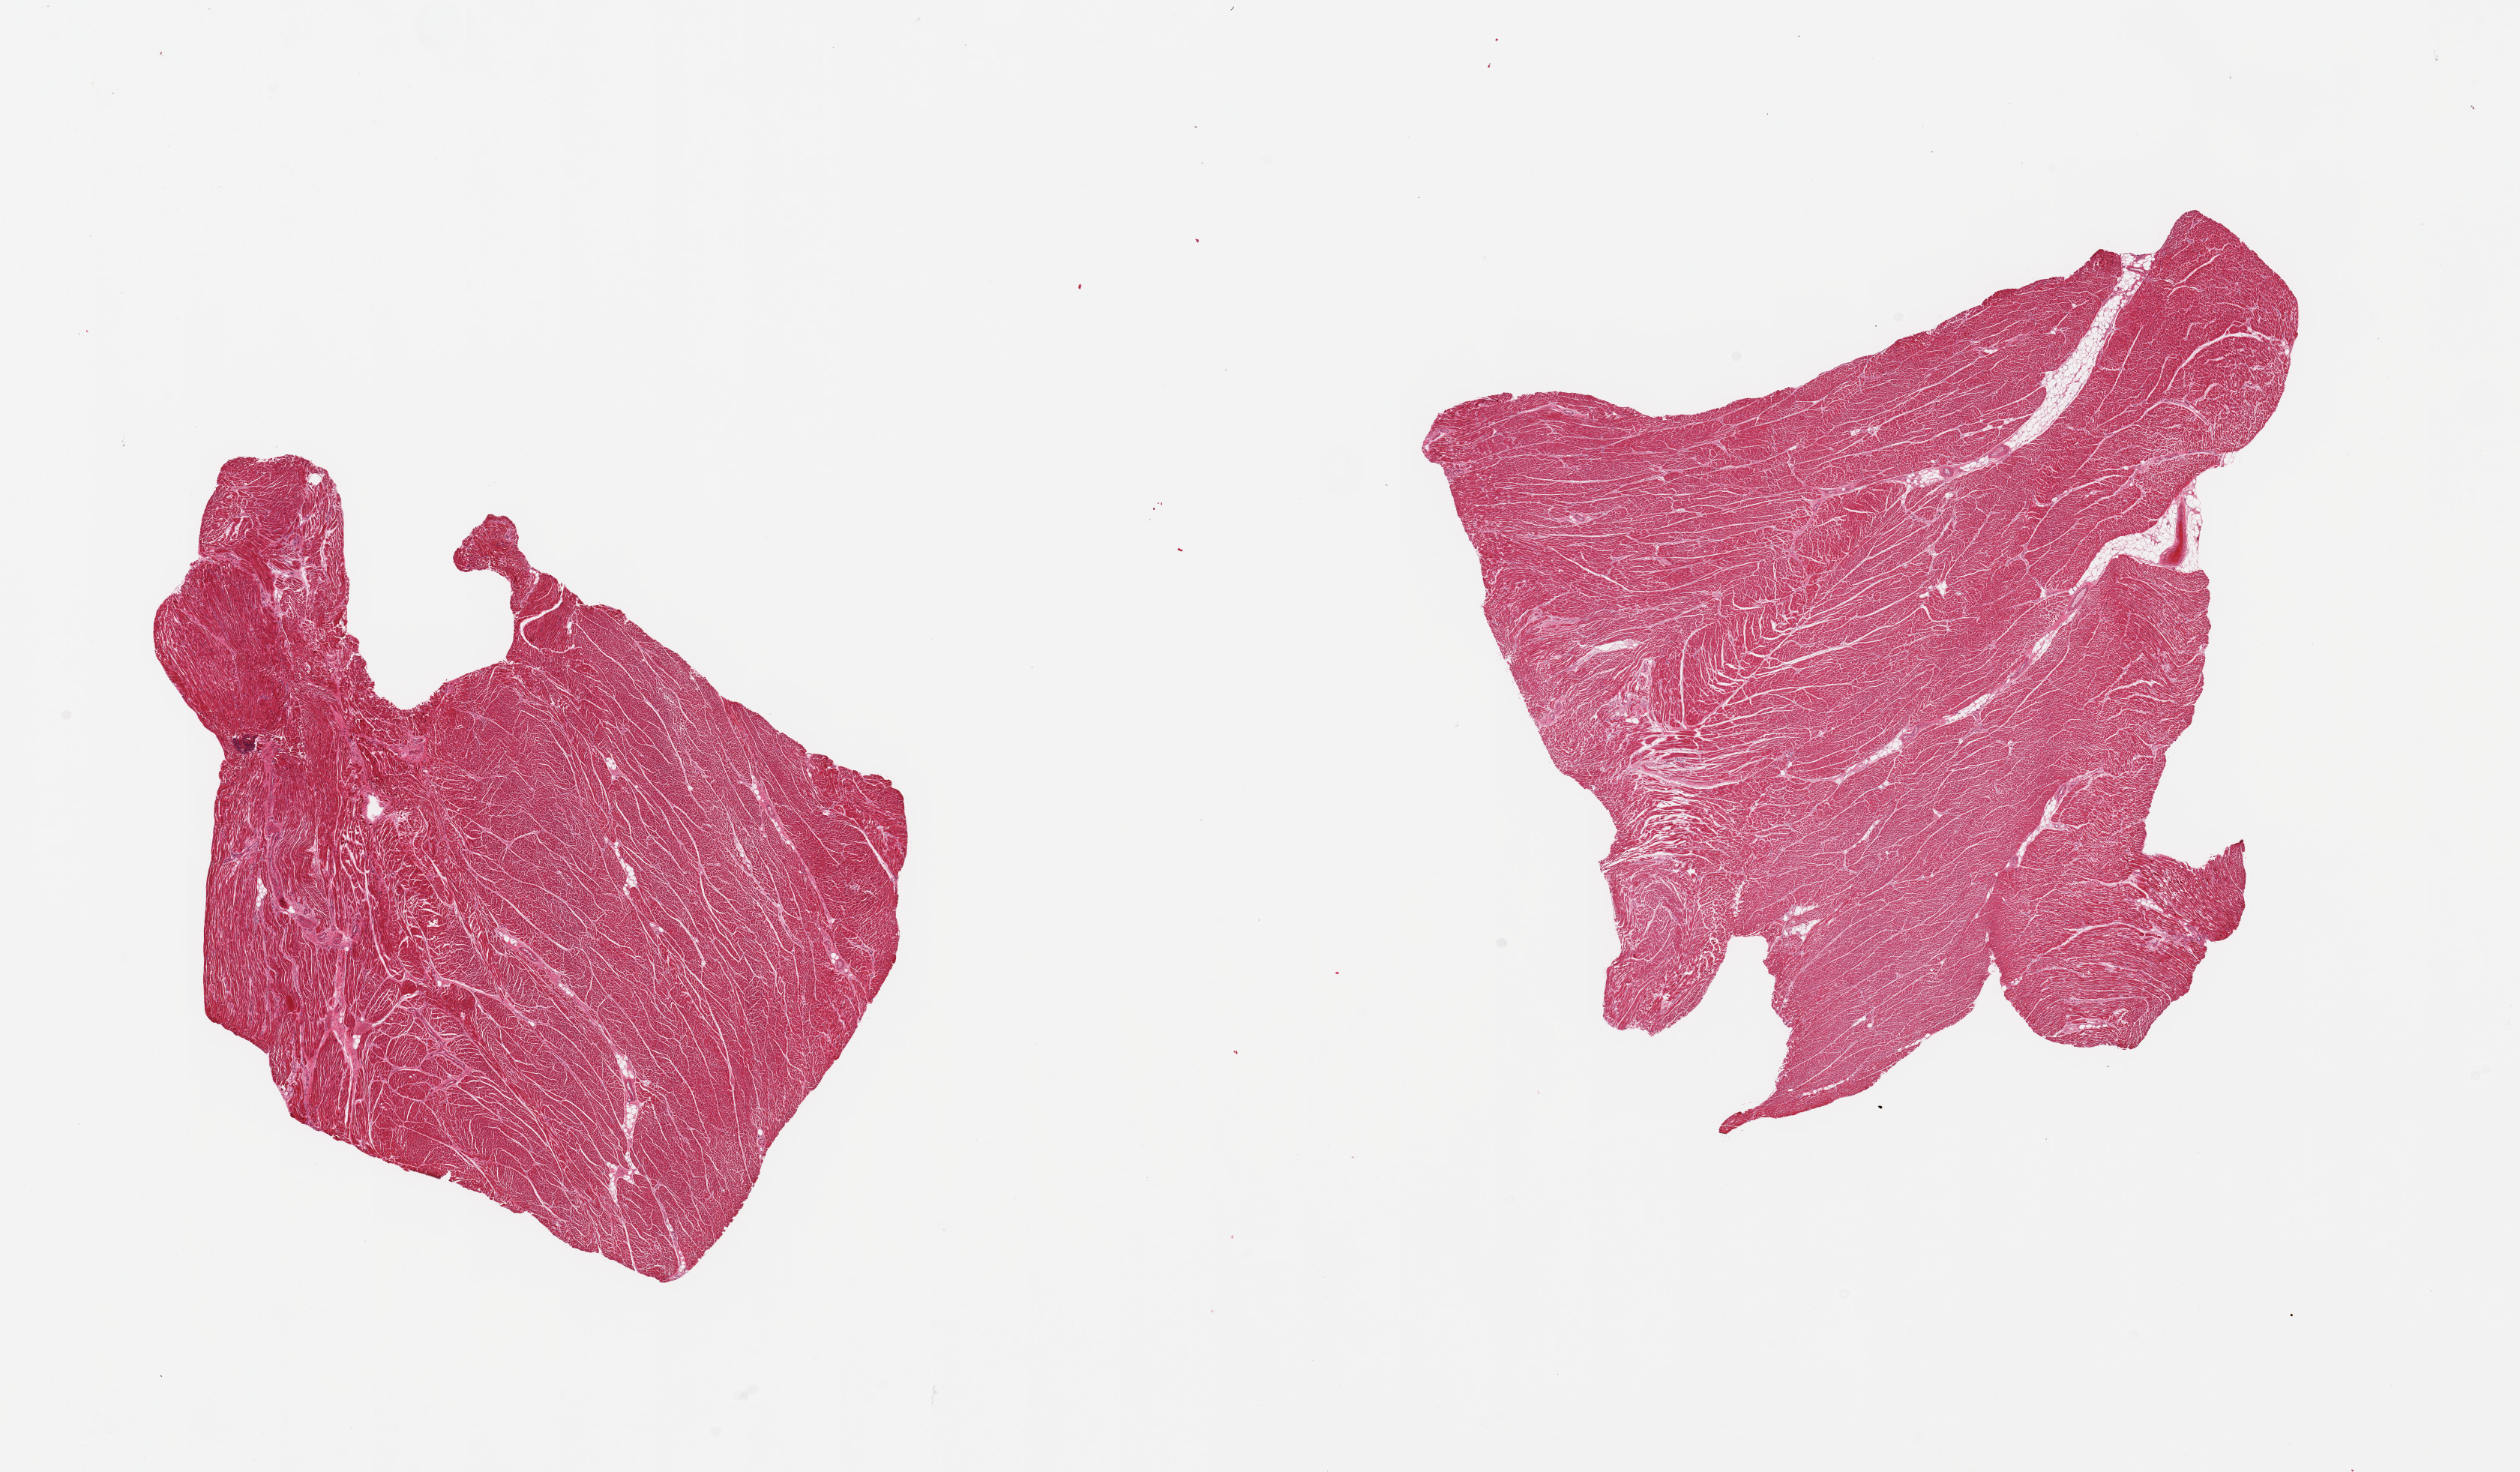
H&E whole-slide image, brightfield, low-resolution overview of the scanned area, about 26.6 x 15.5 mm (from a 20x scan); PAXgene-fixed paraffin-embedded (PFPE) section; section of heart (target tissue); donor tissue sample. Male donor.
Pathologist's review note for this sample: 2 pieces; some interstitial fibrosis; one with minimal internal fat.